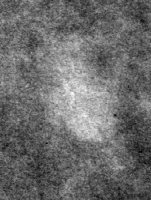
Crop from a digitized film mammogram around one marked abnormality, left breast, MLO view, BI-RADS breast density category 1 (scale 1–4).
- Finding: mass, shape lymph node, margins circumscribed; BI-RADS assessment category 2; subtlety rating 4 on a 1 (subtle) to 5 (obvious) scale; benign without callback (not worked up further).